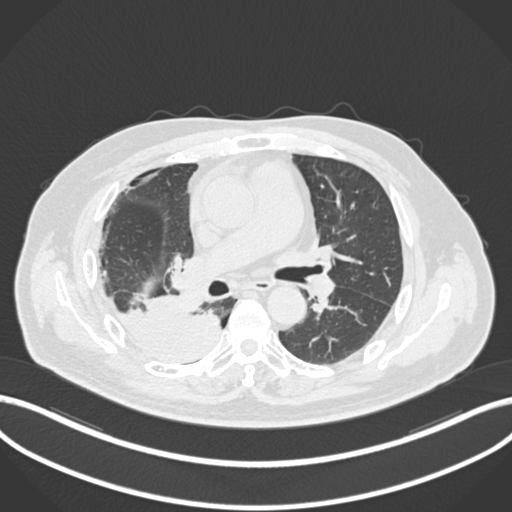
Chest CT, one axial slice; slice 106 of 218 in the series (ordered by position); reconstruction kernel B30f; 120 kVp; lung window (W 1500 / L -600 HU); 1 mm slice thickness; 512 × 512 image matrix, field of view 400 × 400 mm. Patient: male, 68 years. From the clinical record (not read from this slice): clinical TNM (as recorded): T2a N0 M0.
Annotated regions visible in this slice (bounding box drawn by a radiologist):
- lung tumour (recorded histology: adenocarcinoma): box from (x=120, y=297) to (x=222, y=363) px